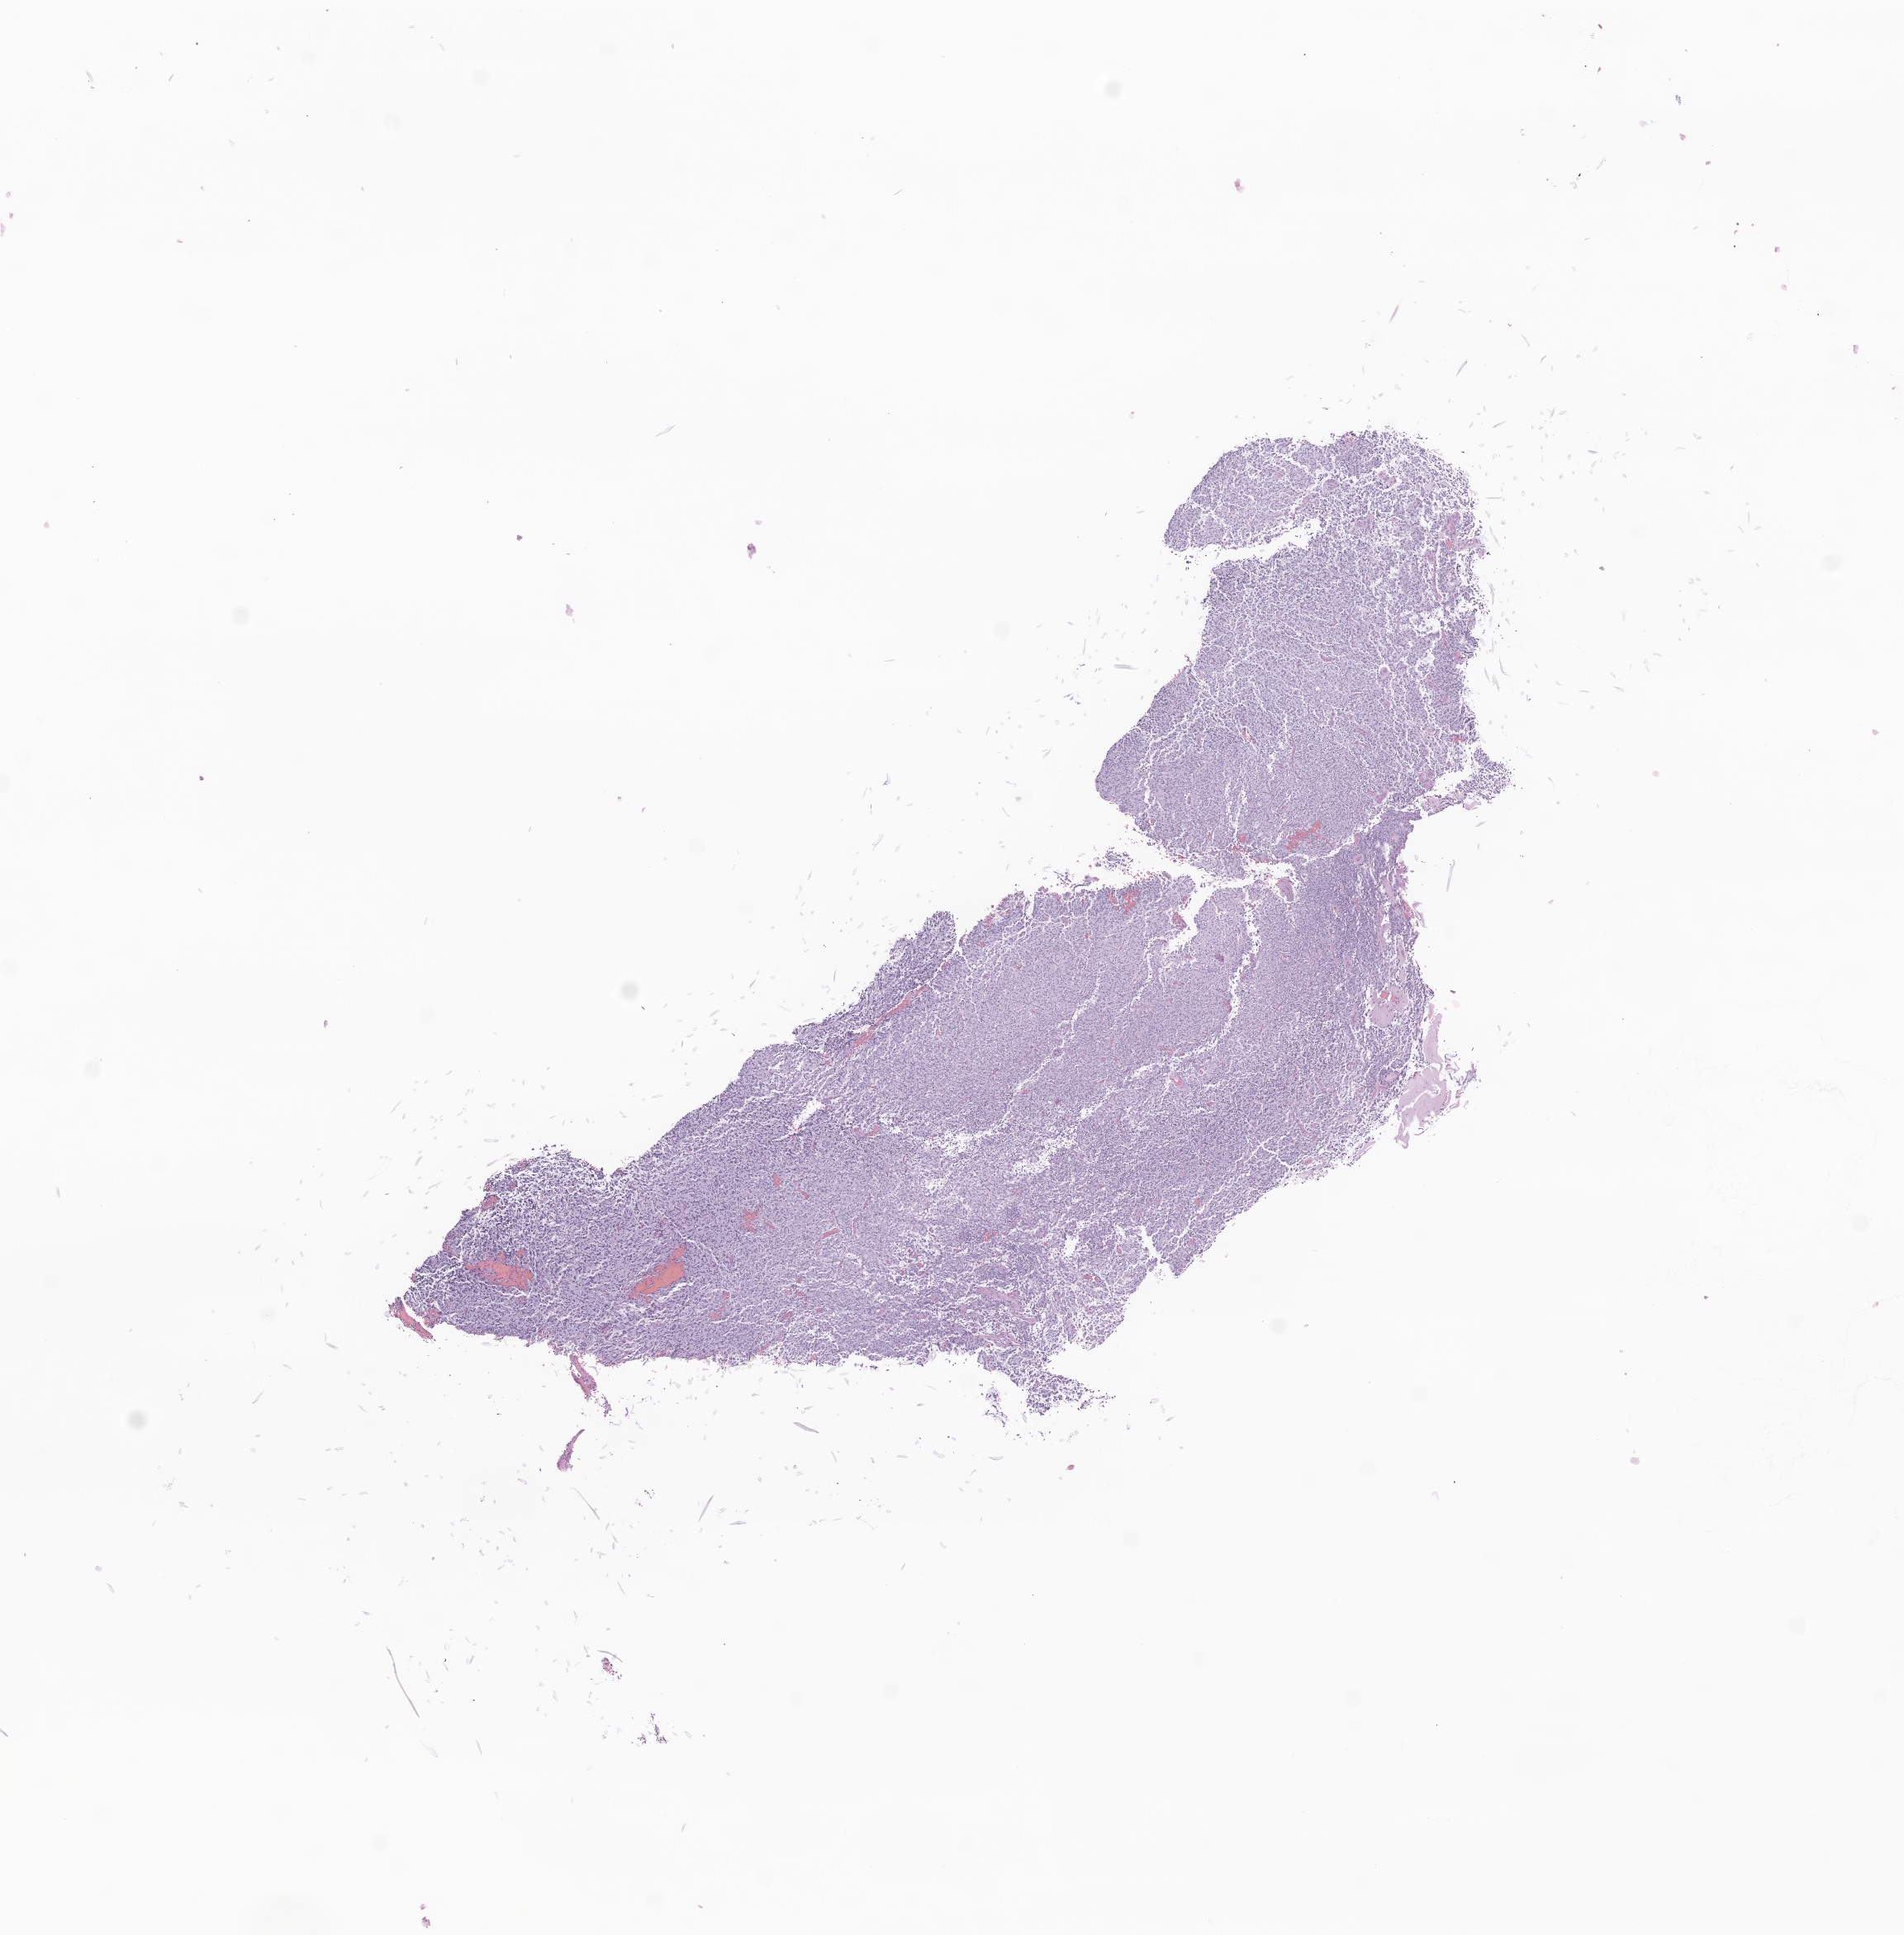
Digitized H&E-stained section of tumor tissue from the cerebellum — shown as a low-resolution overview of the whole scanned area (about 9.7 x 9.9 mm). Formalin-fixed paraffin-embedded section. Patient: male, age 258 months (21 years 6 months).
Recorded diagnosis: Glioblastoma, NOS.